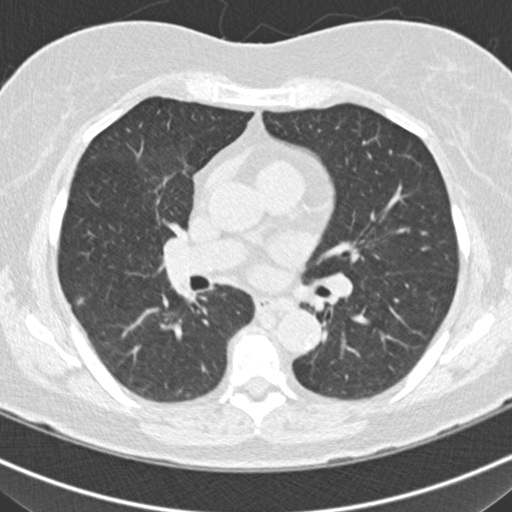
Low-dose screening chest CT, one axial slice; position 103 of 160 along the scan axis; reconstruction kernel B30f; lung window (W 1500 / L -600 HU); 2 mm slice thickness; 512 × 512 image matrix, field of view 316 × 316 mm.
Annotated regions visible in this slice (outlined manually by an expert reader):
- lesion 2 (tumor, middle lobe of right lung): box from (x=77, y=298) to (x=83, y=305) px